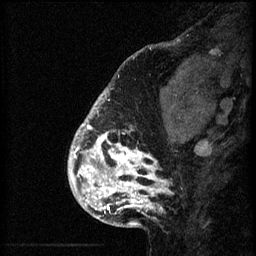
Breast MRI (dynamic contrast-enhanced), one sagittal slice. Slice 16 of 60 in the series (ordered by position). 3 images stored at this slice position (order not interpretable as contrast timing). 1.5 T. TE 4.2 ms, TR 8.2 ms. 256 × 256 image matrix, field of view 180 × 180 mm. Patient: female, 41 years.
Annotated regions visible in this slice (semi-automatically segmented with operator editing):
- analysis volume of interest (the breast-tissue region the enhancement analysis was run in; not a lesion): bounding box (x1, y1, x2, y2) in pixels: (72, 108, 176, 205)
- tumour enhancement mask (voxels above the 70 % enhancement threshold inside the analysis volume of interest): (72, 108, 168, 205)